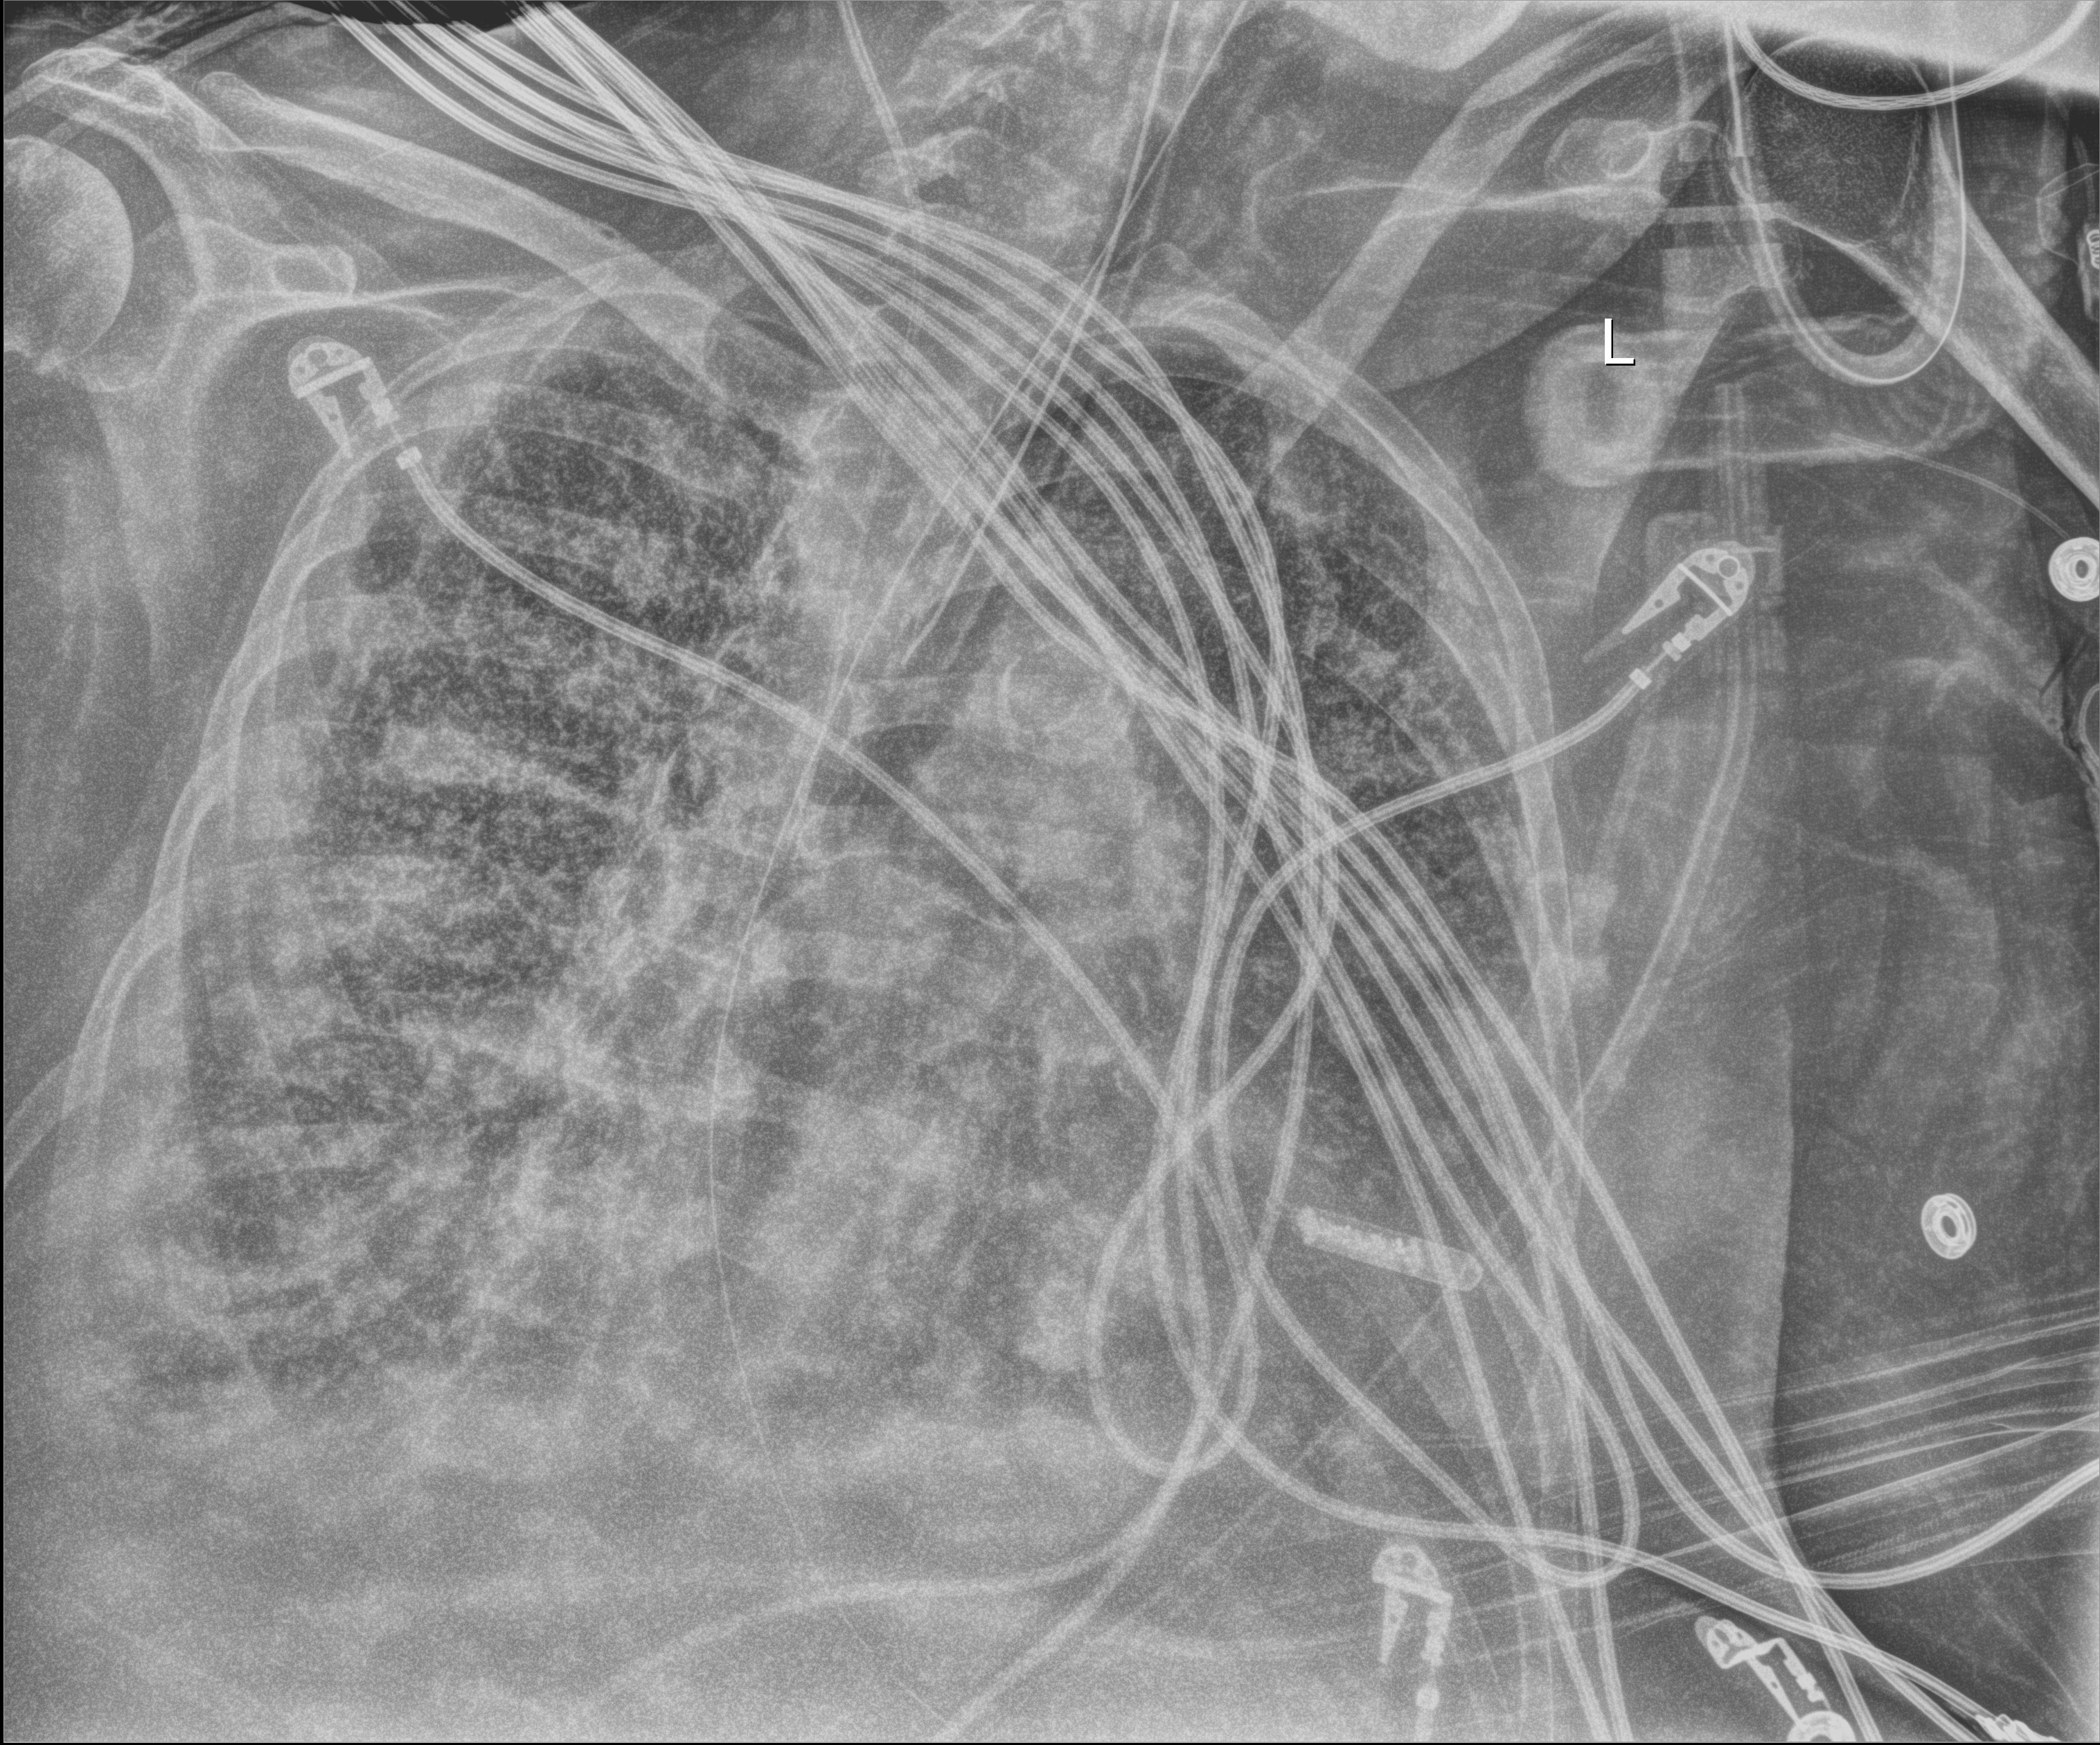
Bedside chest radiograph (digital radiography), anteroposterior (AP) projection. Female patient hospitalised with COVID-19, age 60–74 years.
Admission-level facts for this patient (not findings on this image; timing relative to this image not recorded): length of hospital stay: 28 days; admitted to intensive care during this hospital stay: yes; mechanically ventilated during this hospital stay: yes.